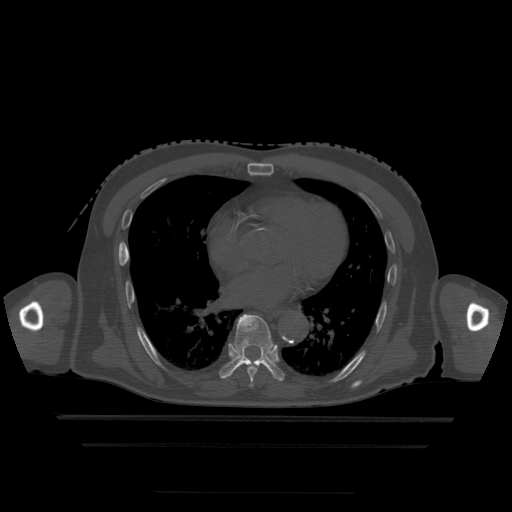
CT including the spine, one axial slice; position 287 of 522 along the scan axis; bone window (W 1800 / L 400 HU); 1.25 mm slice thickness; 512 × 512 image matrix. Patient age 68 years. Case-level facts recorded for this patient, not image findings: primary cancer: urothelial.
Structures marked on this image (semi-automatic segmentation, software-assisted and operator-edited):
- T6 vertebra: bounding box [x1, y1, x2, y2] px = [250, 382, 253, 387]
- T7 vertebra: [248, 365, 259, 383]
- T8 vertebra: [220, 315, 285, 382]